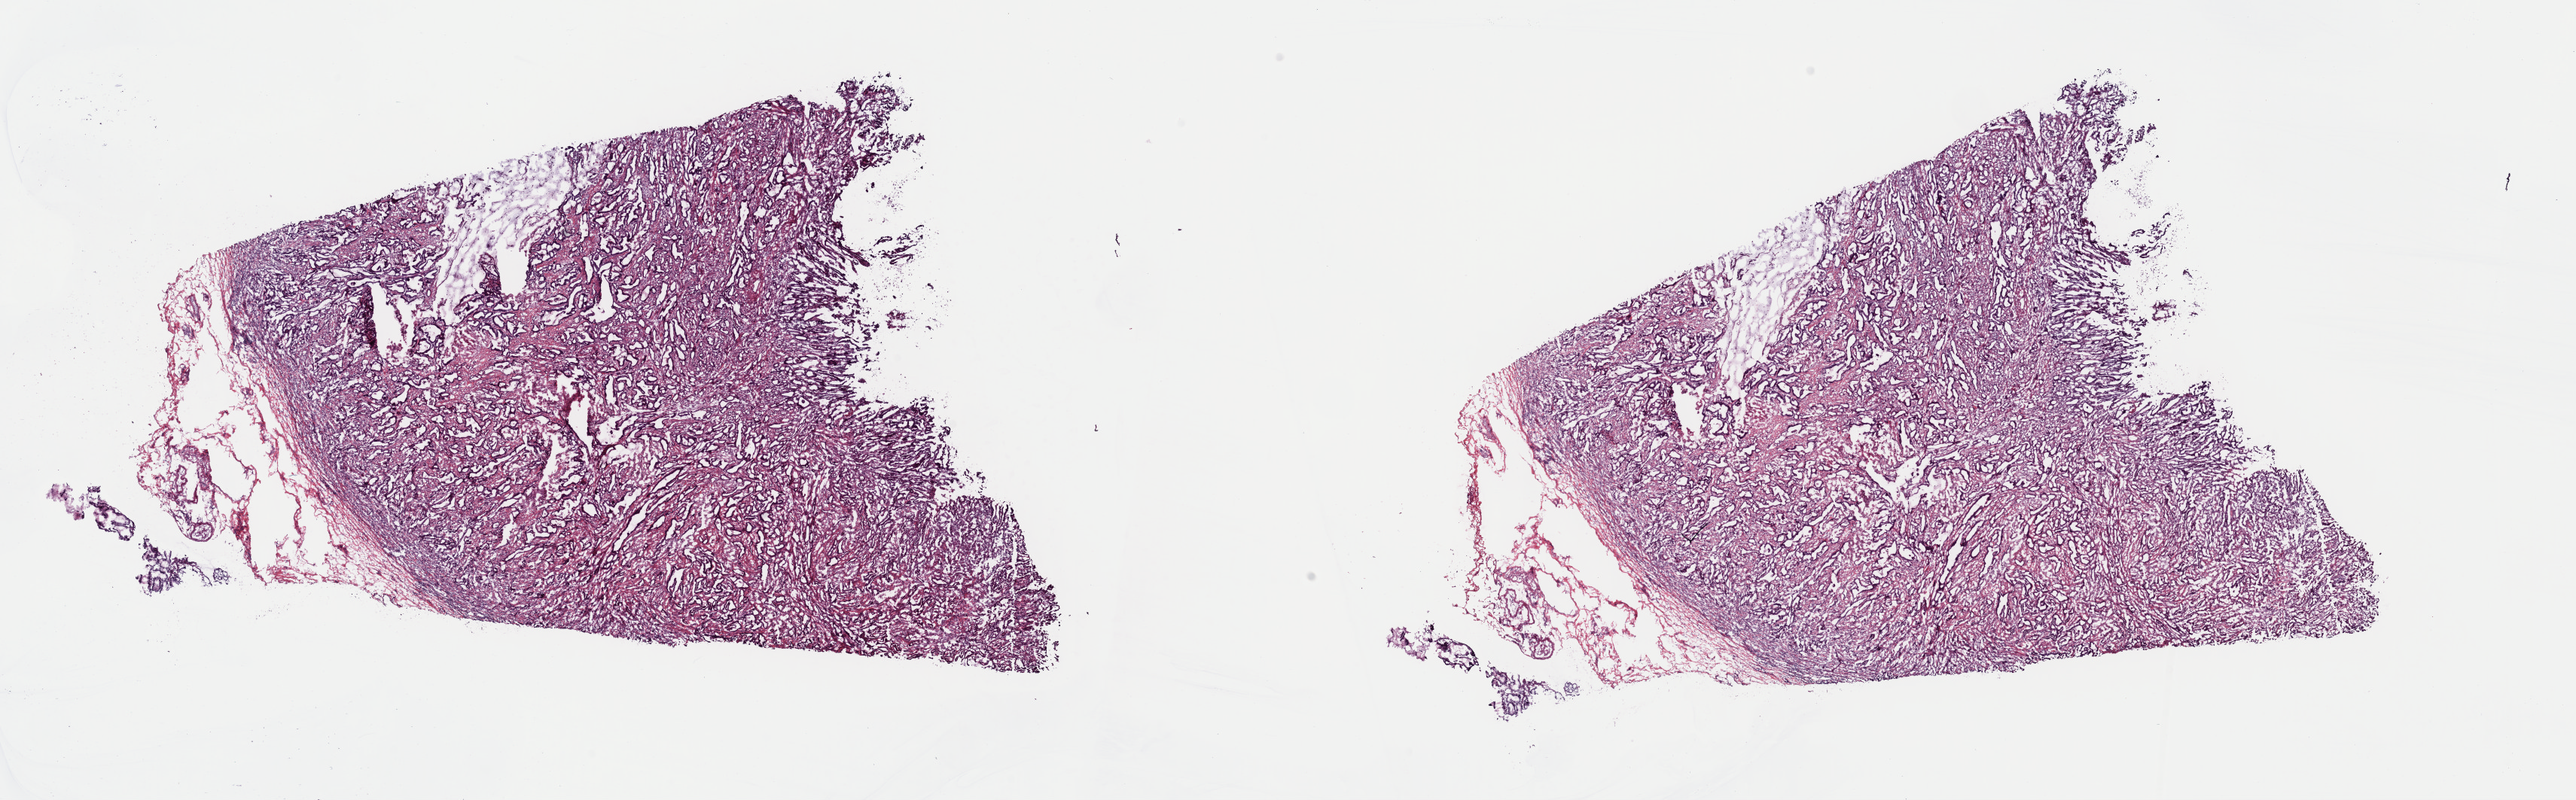
Whole-slide histology image, H&E — low-resolution overview of the scanned area, about 27.0 x 8.4 mm. Frozen section. Primary tumour sample from the stomach. Male, age 60 years at initial diagnosis. Histologic grade: G2 (moderately differentiated). Pathologist review of this section (percent, as recorded): tumour cells 60%, tumour nuclei 75%, normal cells 0%, stromal cells 38%, necrosis 2%. Inflammatory infiltration, as recorded: lymphocyte infiltration 0%, monocyte infiltration 0%, neutrophil infiltration 0%.
Diagnosis: Adenocarcinoma, NOS (fundus of stomach). AJCC pathologic stage: IB (7th edition). TNM: T2 N0 M0.